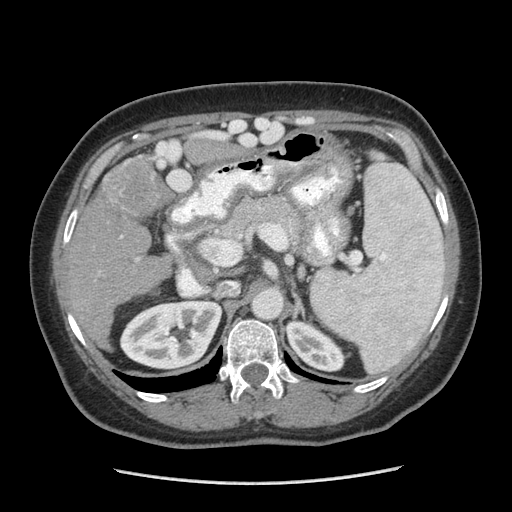
Contrast-enhanced abdominal CT (liver protocol), one axial slice. Slice 147 of 185 in the series (ordered by position). Reconstruction kernel STANDARD. Soft-tissue window (W 400 / L 40 HU). 2.5 mm slice thickness. 512 × 512 image matrix, field of view 360 × 360 mm. From the clinical record (not read from this slice): diagnosis: hepatocellular carcinoma (patient treated with transarterial chemoembolisation; whether this scan precedes or follows treatment is not stated here); TNM stage (as recorded): Stage-I; Child-Pugh class: A; tumour differentiation: poorly differentiated; tumour nodularity: uninodular.
Outlined on this slice (semi-automatically segmented with operator editing):
- liver parenchyma outside the tumour (the mass and vessels are separate outlines, so this box may not span the whole liver): bounding box [x1, y1, x2, y2] px = [64, 154, 172, 338]
- mass: [99, 156, 169, 217]
- liver vessels: [121, 236, 139, 260]